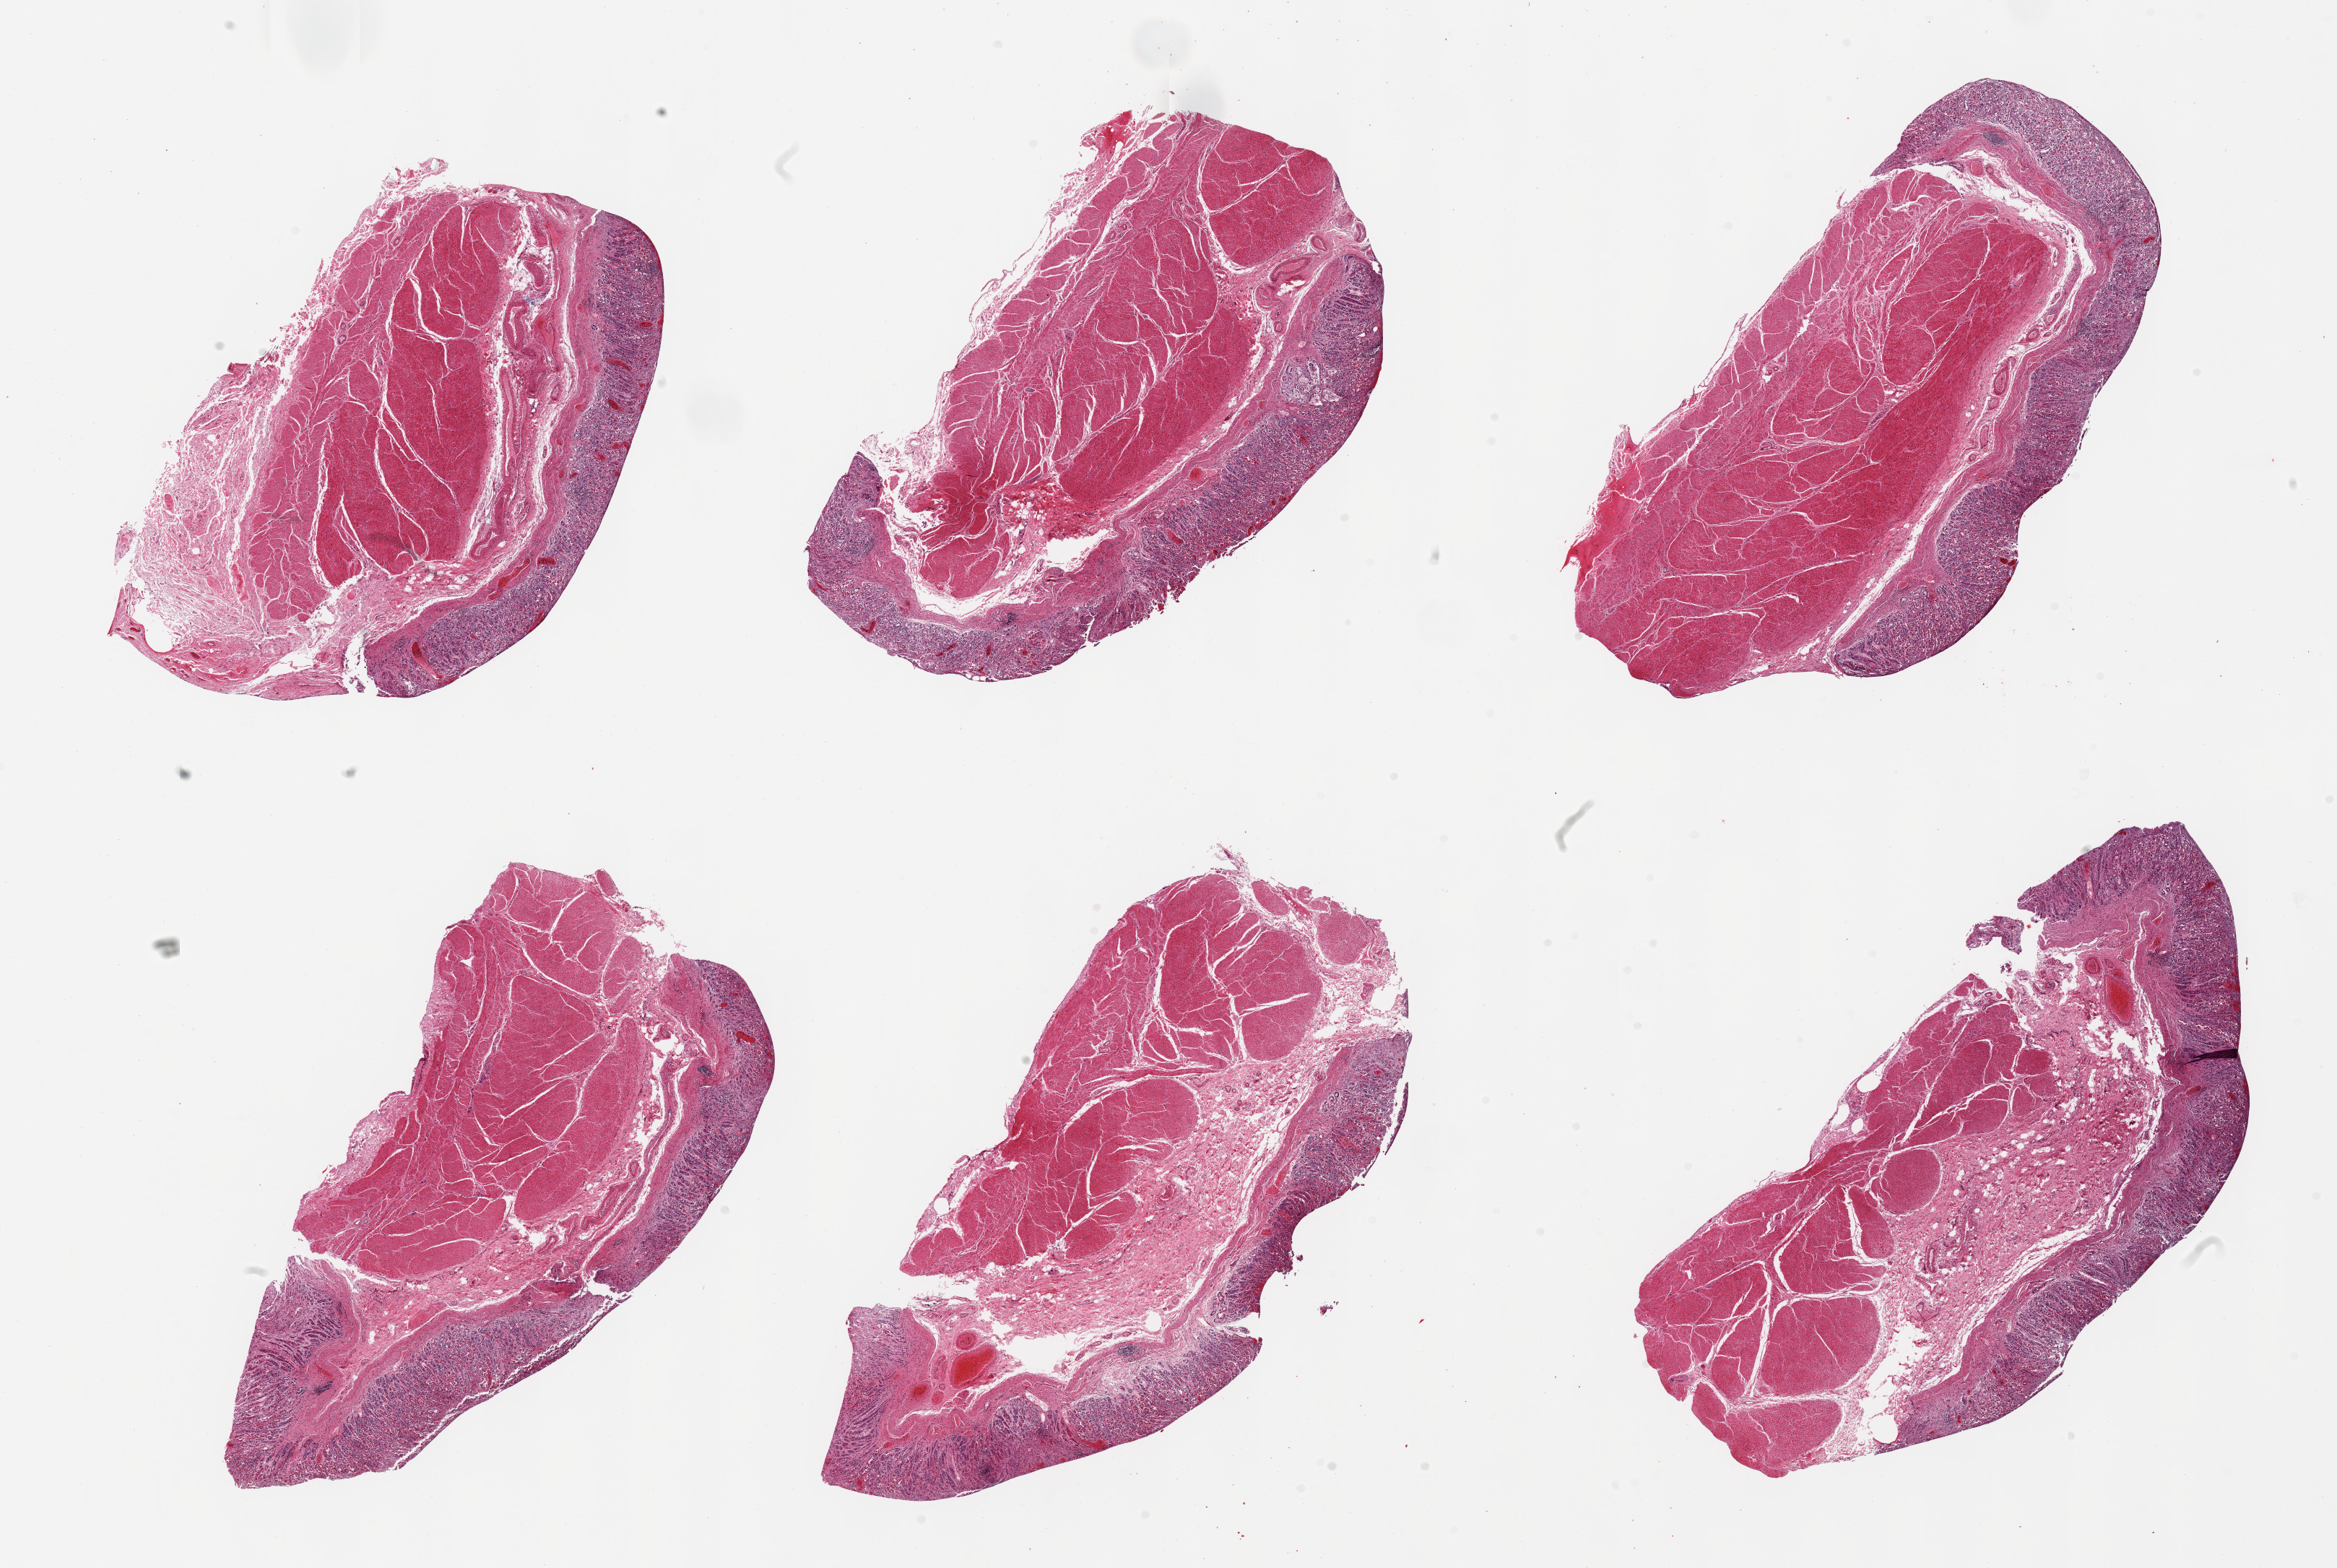
Haematoxylin and eosin whole-slide image — whole scanned area (about 25.6 x 17.2 mm, acquisition: 20x scan) shown as a low-resolution overview. PAXgene-fixed, paraffin-embedded tissue. Target tissue: stomach. Donor tissue sample. Male donor.
* review note (as recorded): 6 pieces, mucosa up to ~0.5mm, moderate-advanced autolysis